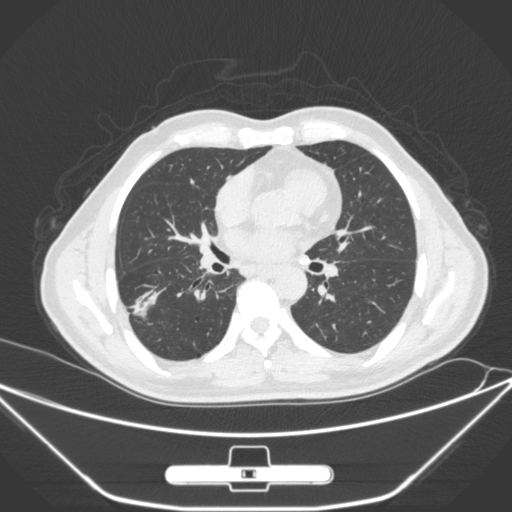
Chest CT, one axial slice. Slice 145 of 310 in the series (ordered by position). 120 kVp. Lung window (W 1500 / L -600 HU). 1 mm slice thickness. 512 × 512 image matrix, field of view 398 × 398 mm. Patient: male, 71 years. From the clinical record (not read from this slice): clinical TNM (as recorded): T1c N0 M0; histopathological grade: G2.
Structures marked on this image (bounding box drawn by a radiologist):
- lung tumour (recorded histology: adenocarcinoma): bounding box <133,282,166,324> (left, top, right, bottom; pixels)